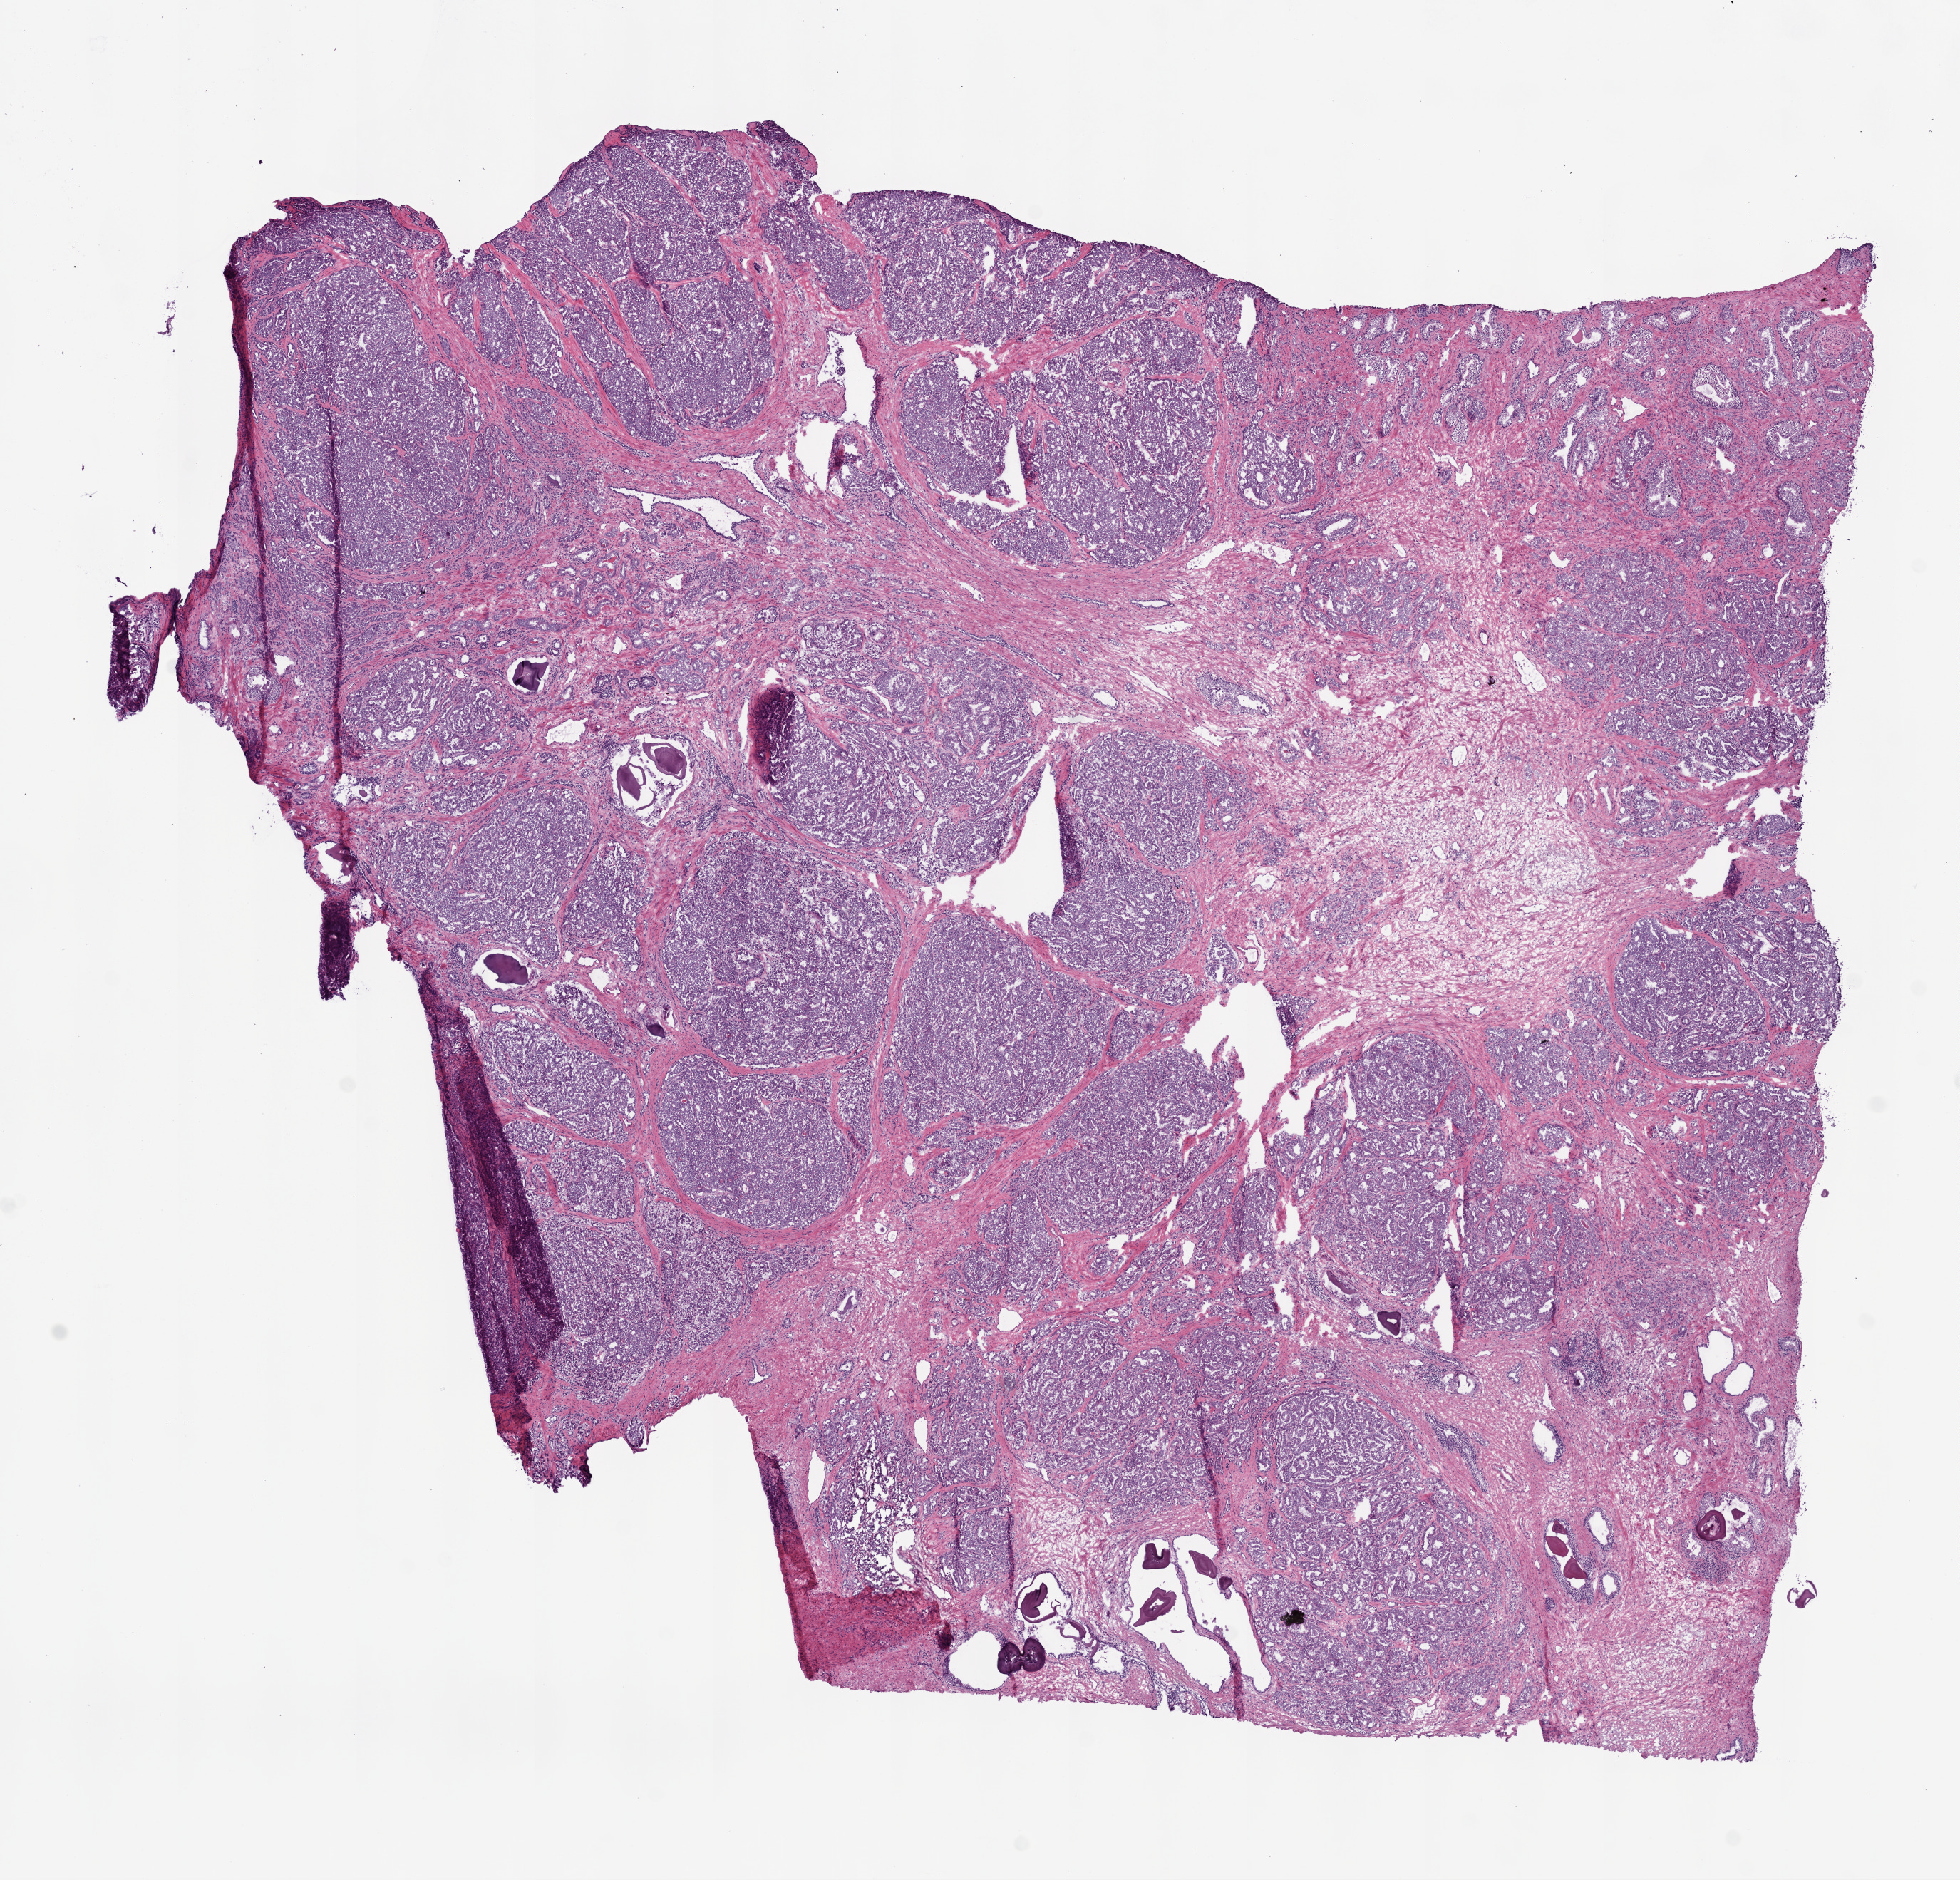
H&E-stained whole-slide image — whole scanned area (about 11.0 x 10.6 mm, slide scanned at 20x) shown as a low-resolution overview. Frozen section. Sample: primary tumour, prostate. Patient: male, age at initial diagnosis 64 years. Gleason score: 8 (4+4). Composition of this section per pathologist review: tumour cells 60%, tumour nuclei 65%, normal cells 15%, stromal cells 25%, necrosis 0%. Inflammatory infiltration, as recorded: lymphocyte infiltration 3%, monocyte infiltration 1%, neutrophil infiltration 0%.
Lymph nodes positive (case pathology): 3 of 12 examined. Diagnosis: Acinar cell carcinoma (prostate gland). Laterality: bilateral.